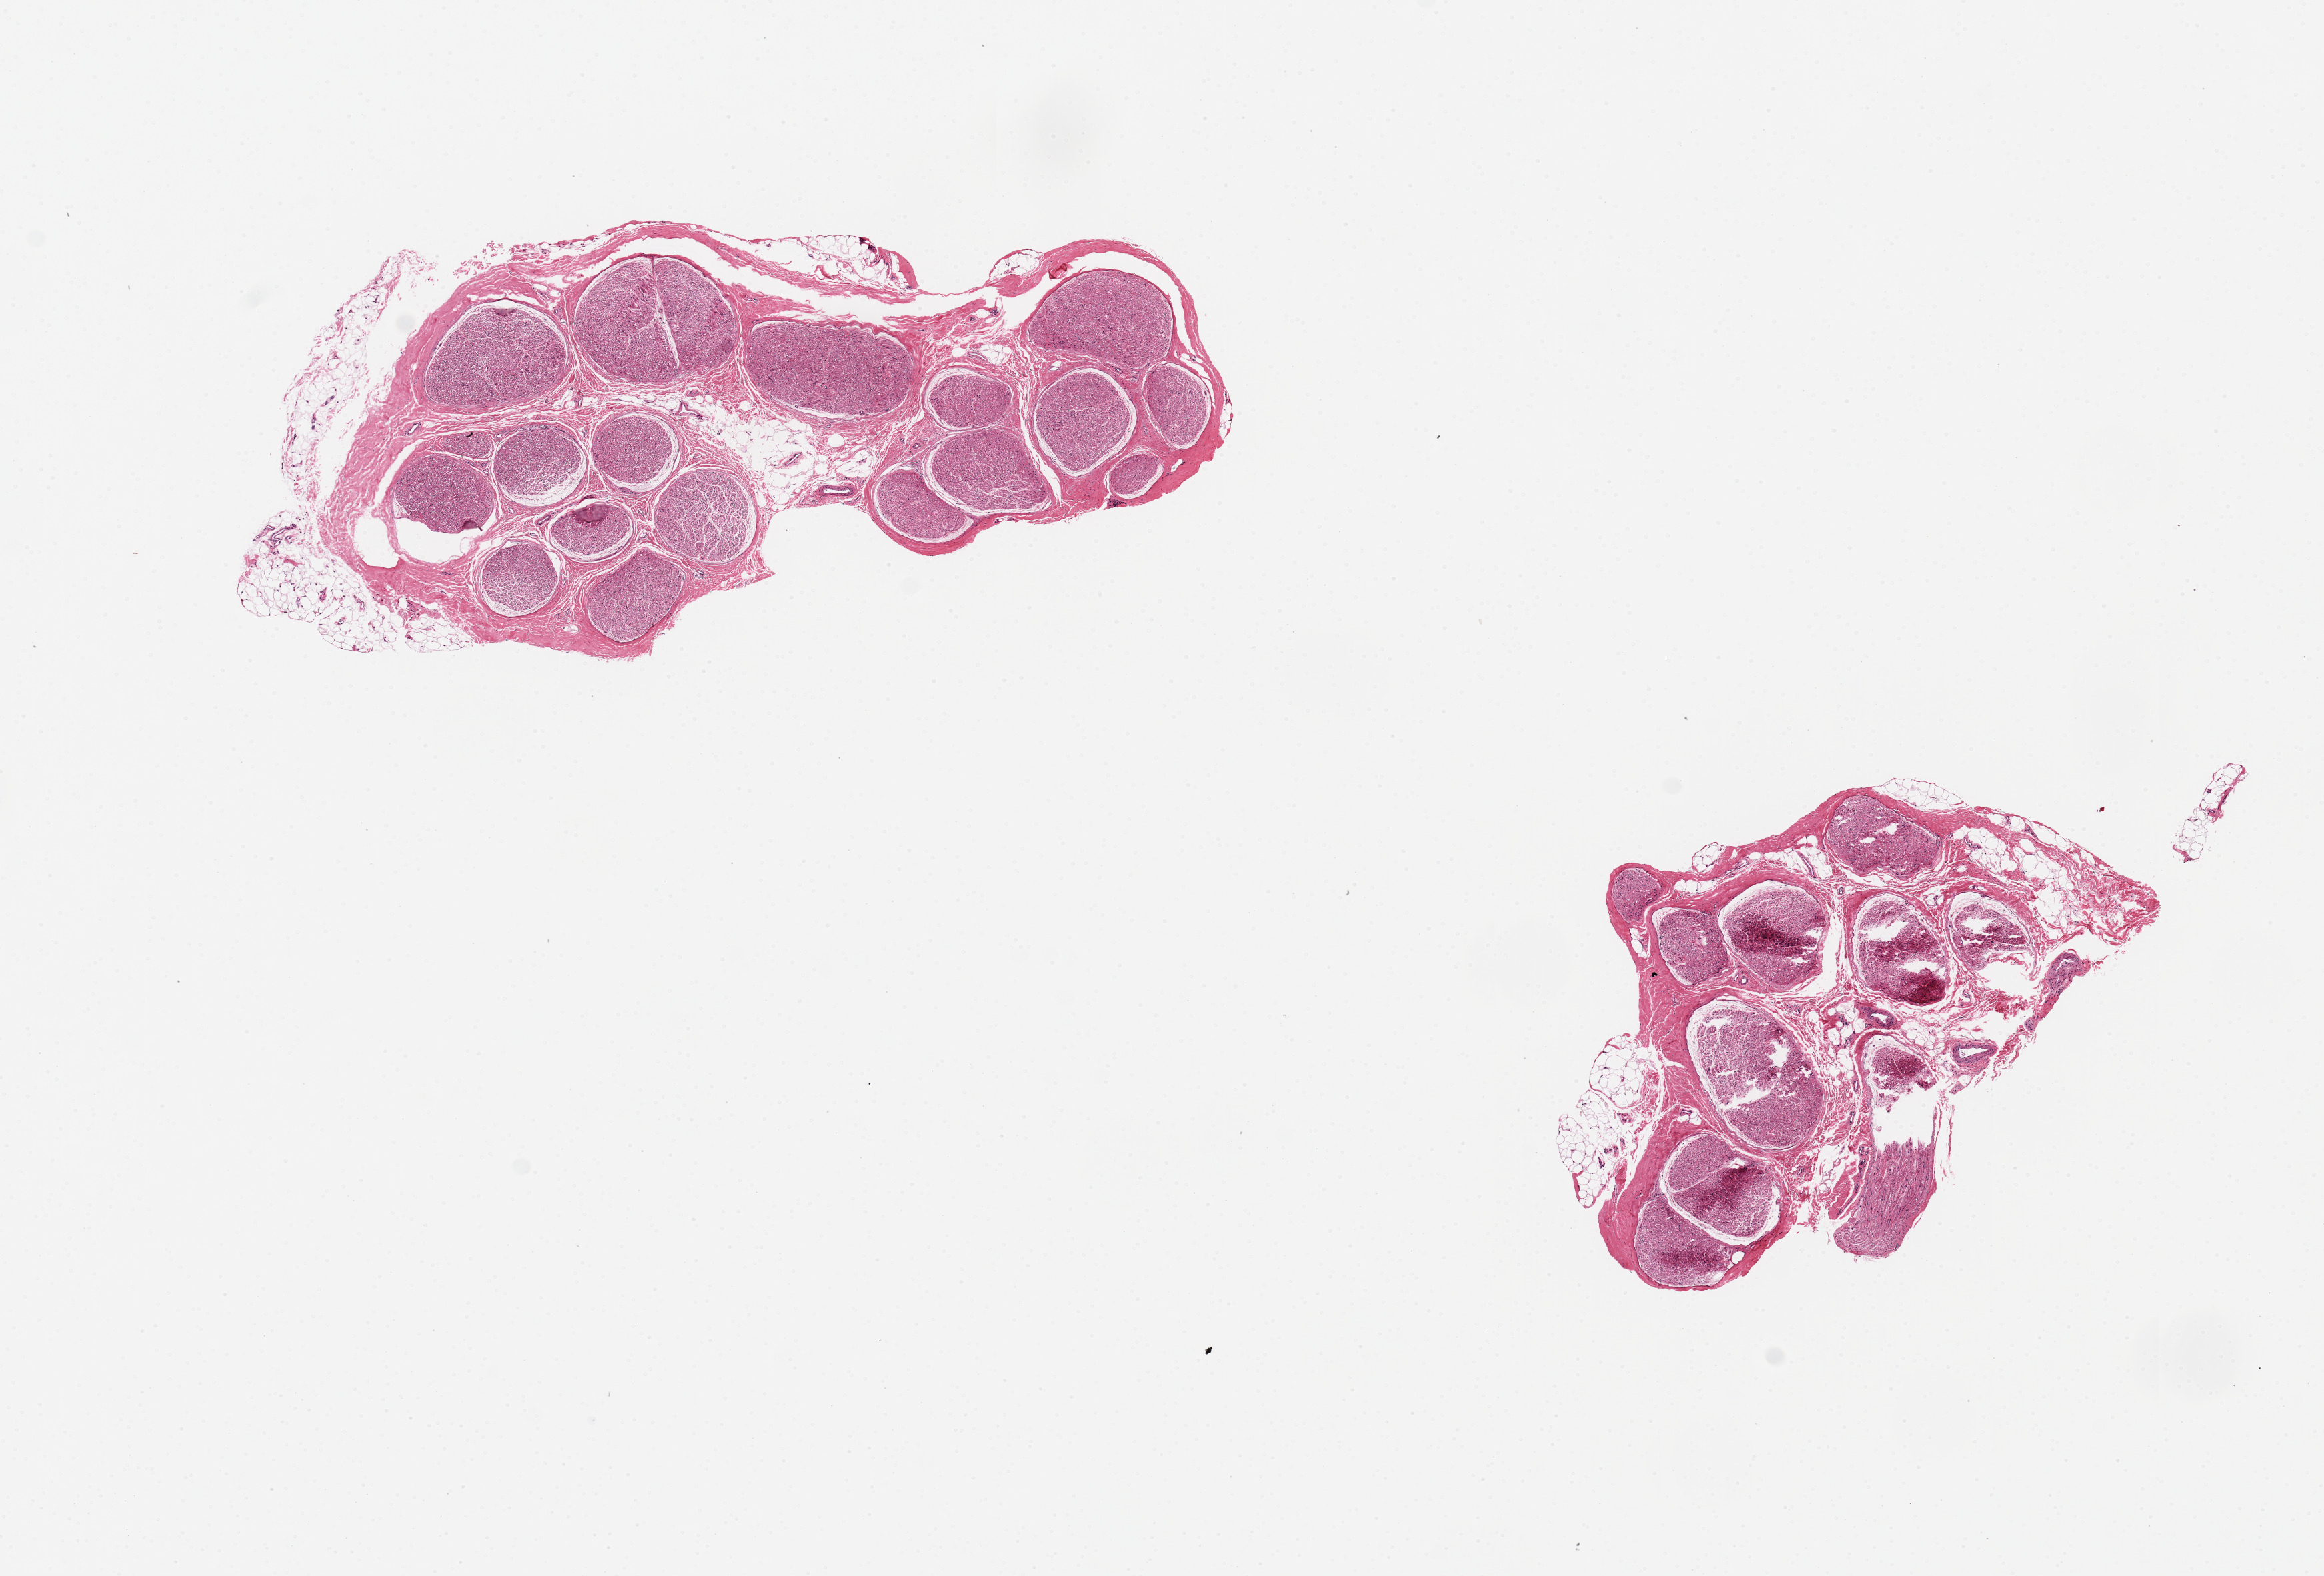
Whole-slide image, haematoxylin and eosin stain, a low-resolution overview of the entire scanned area, about 13.8 x 9.3 mm, PAXgene-fixed, paraffin-embedded tissue, target tissue: tibial nerve, tissue donor sample.
Pathologist's review note for this sample: 2 pieces, 3x2.5 & 5.5x2mm;~10% external adipose.